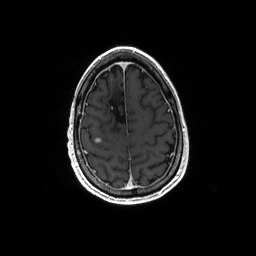
Brain MRI from a brain-tumour surgery series, one axial slice; T1-weighted post-contrast; 1 mm slice thickness; 256 × 256 image matrix, field of view 256 × 256 mm. Case-level facts recorded for this patient, not image findings: histopathology: Astrocytoma; WHO grade: 4; IDH mutation: yes; tumour location: Right Frontal.
Outlined on this slice (expert manual segmentation):
- tumour: bounding box <96,139,100,142> (left, top, right, bottom; pixels)